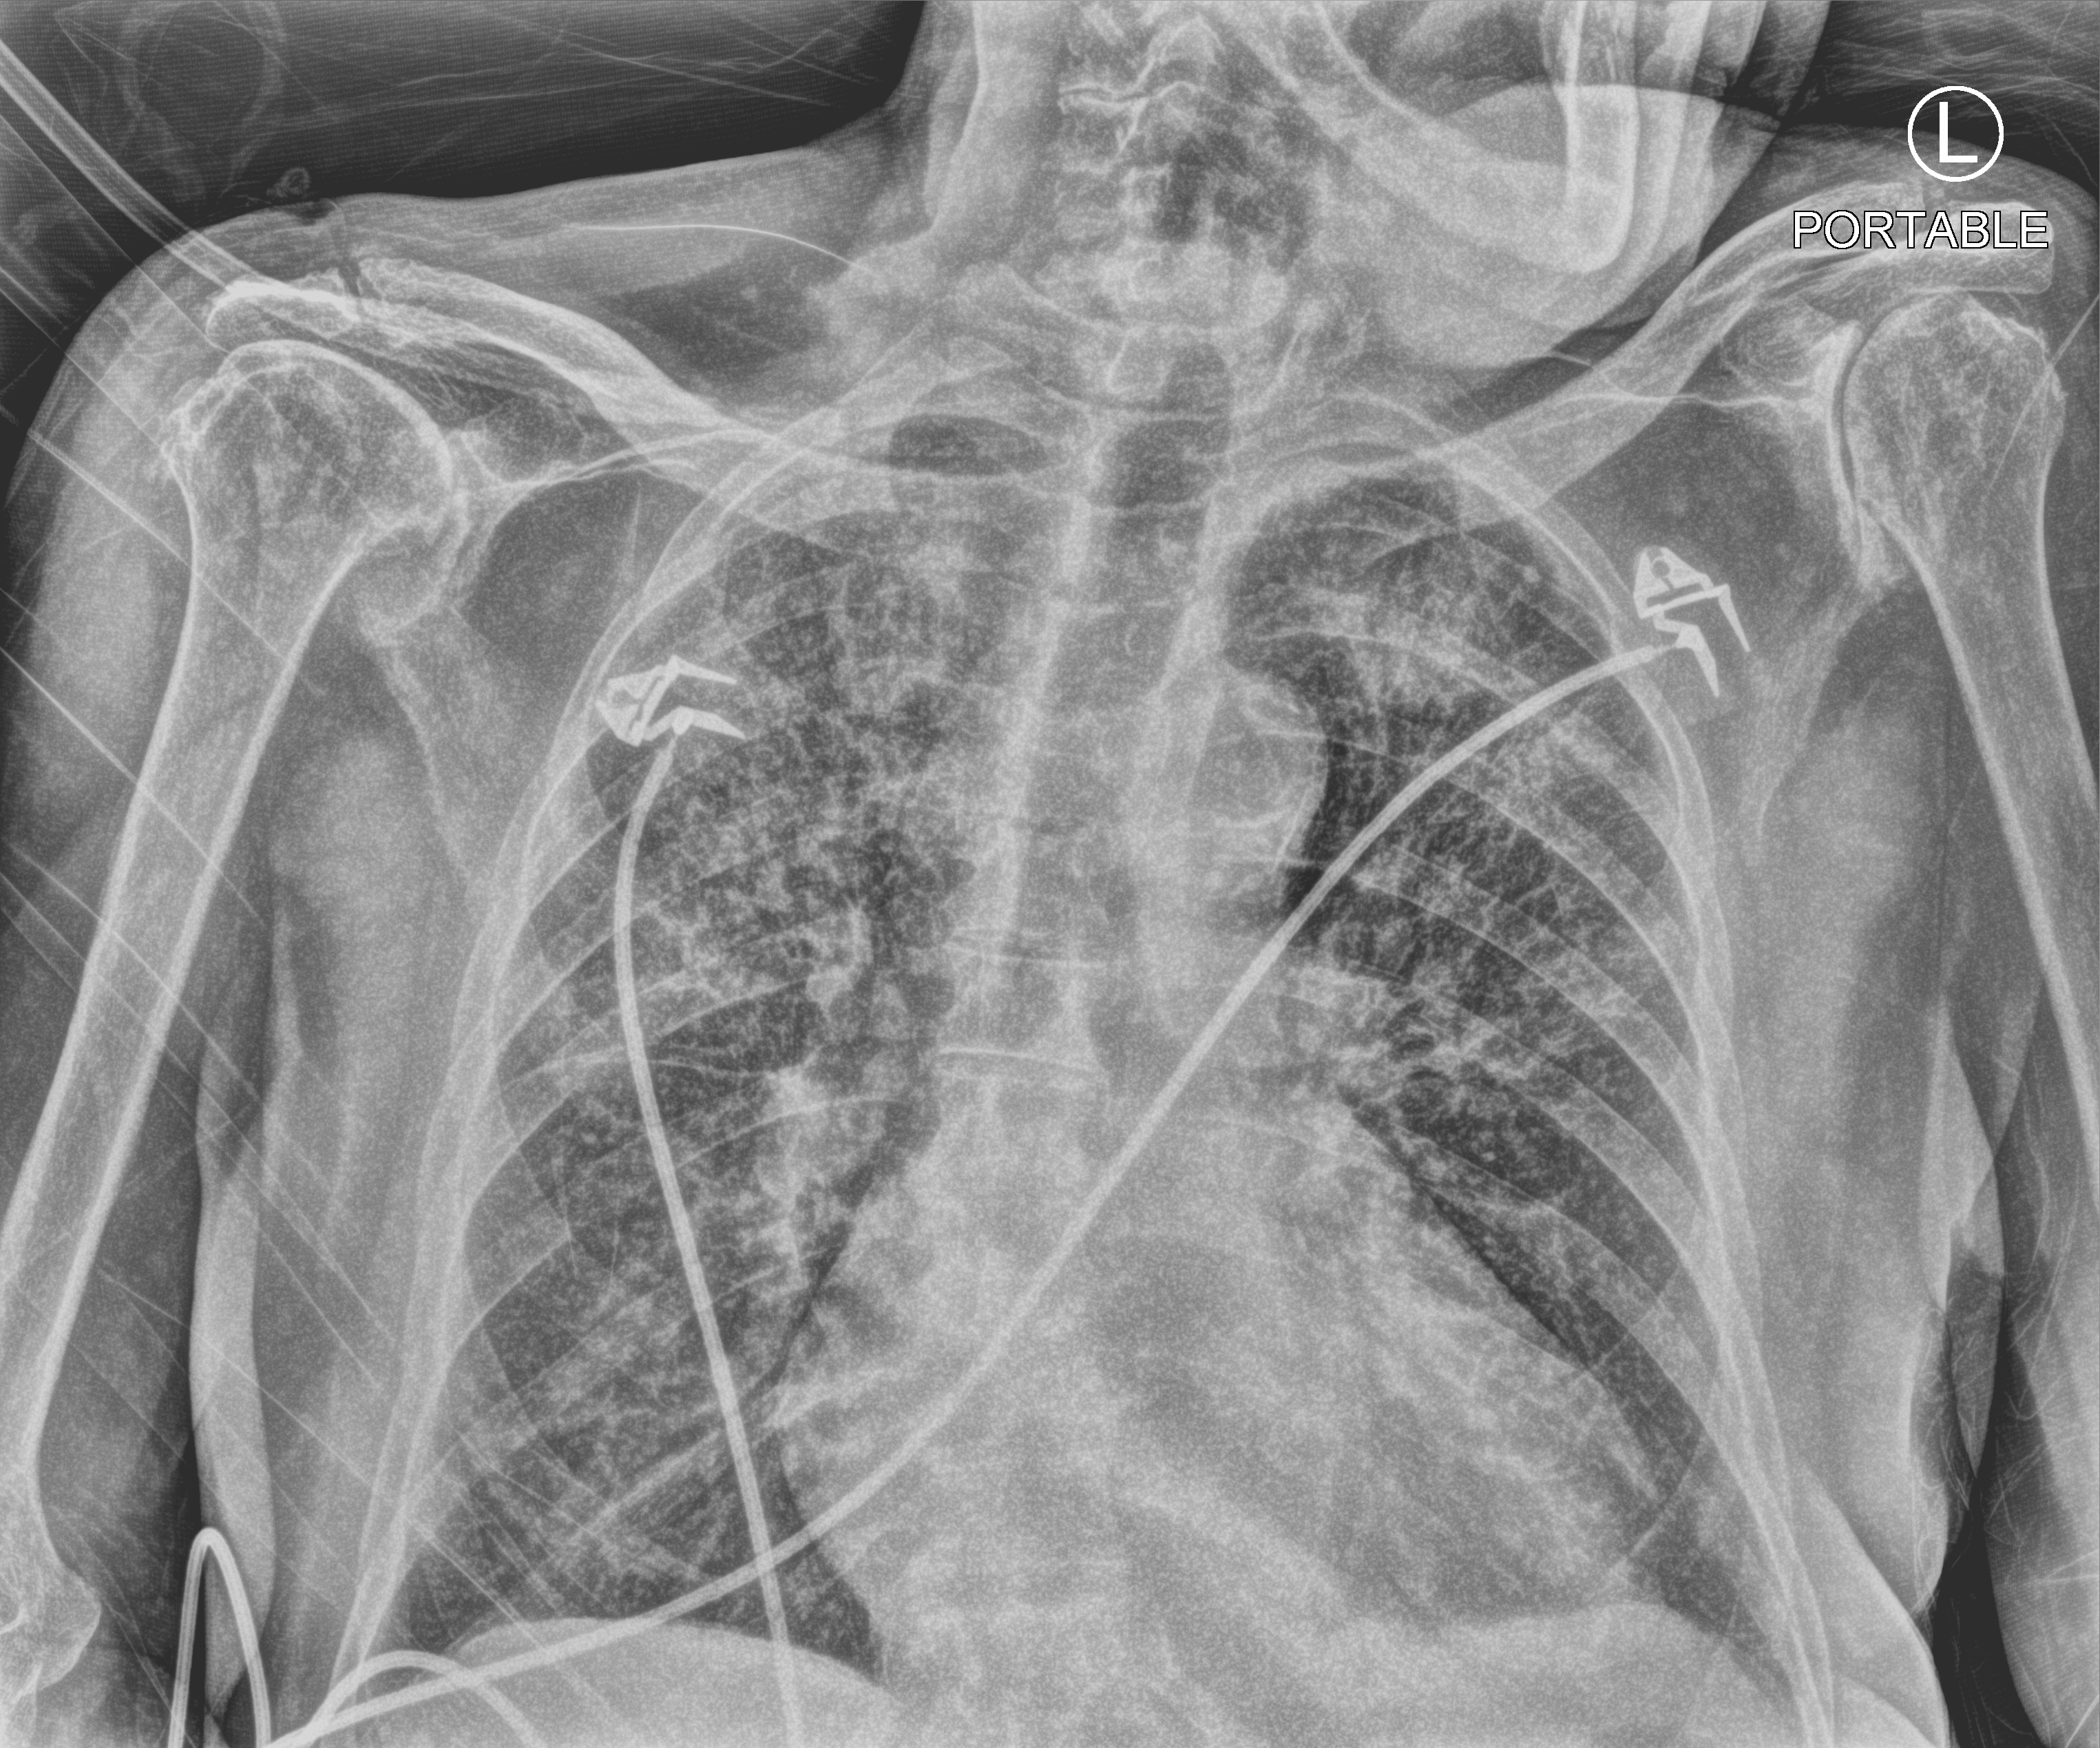
Portable chest radiograph. Patient hospitalised with COVID-19; male, aged 75–90 years.
Admission-level facts for this patient (not findings on this image; timing relative to this image not recorded):
- other chronic lung disease (admission record): no
- admitted to intensive care during this hospital stay: no
- mechanically ventilated during this hospital stay: no